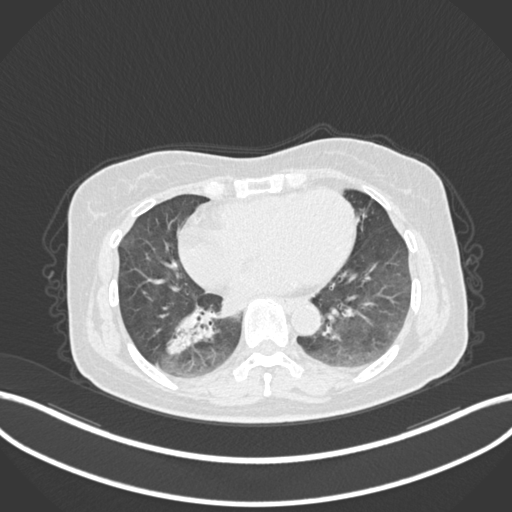
Chest CT, one axial slice. Slice 54 of 222 in the series (ordered by position). 120 kVp. Lung window (W 1500 / L -600 HU). 1 mm slice thickness. 512 × 512 image matrix. Female patient, age 67 years. Case-level facts recorded for this patient, not image findings: clinical TNM (as recorded): T1c N1 M0.
Outlined on this slice (rectangle marked by the reading radiologist):
- lung tumour (recorded histology: adenocarcinoma): bounding box (x1, y1, x2, y2) in pixels: (159, 300, 219, 362)